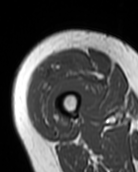
MRI of an extremity soft-tissue mass, one axial slice; slice 25 of 99 in the series (ordered by position); MR volume resampled by the dataset authors to the PET/CT grid (not the native acquisition matrix); 3.27 mm slice thickness; 138 × 172 image matrix, field of view 135 × 168 mm. Female patient. Case-level facts recorded for this patient, not image findings: histological type: pleiomorphic undifferentiated sarcoma; grade: high; site of the primary tumour: right quadricep.
Structures marked on this image (expert contour drawn on MRI and transferred to this co-registered scan by the dataset authors):
- gross tumour volume including surrounding oedema: bounding box <30,52,93,124> (left, top, right, bottom; pixels)